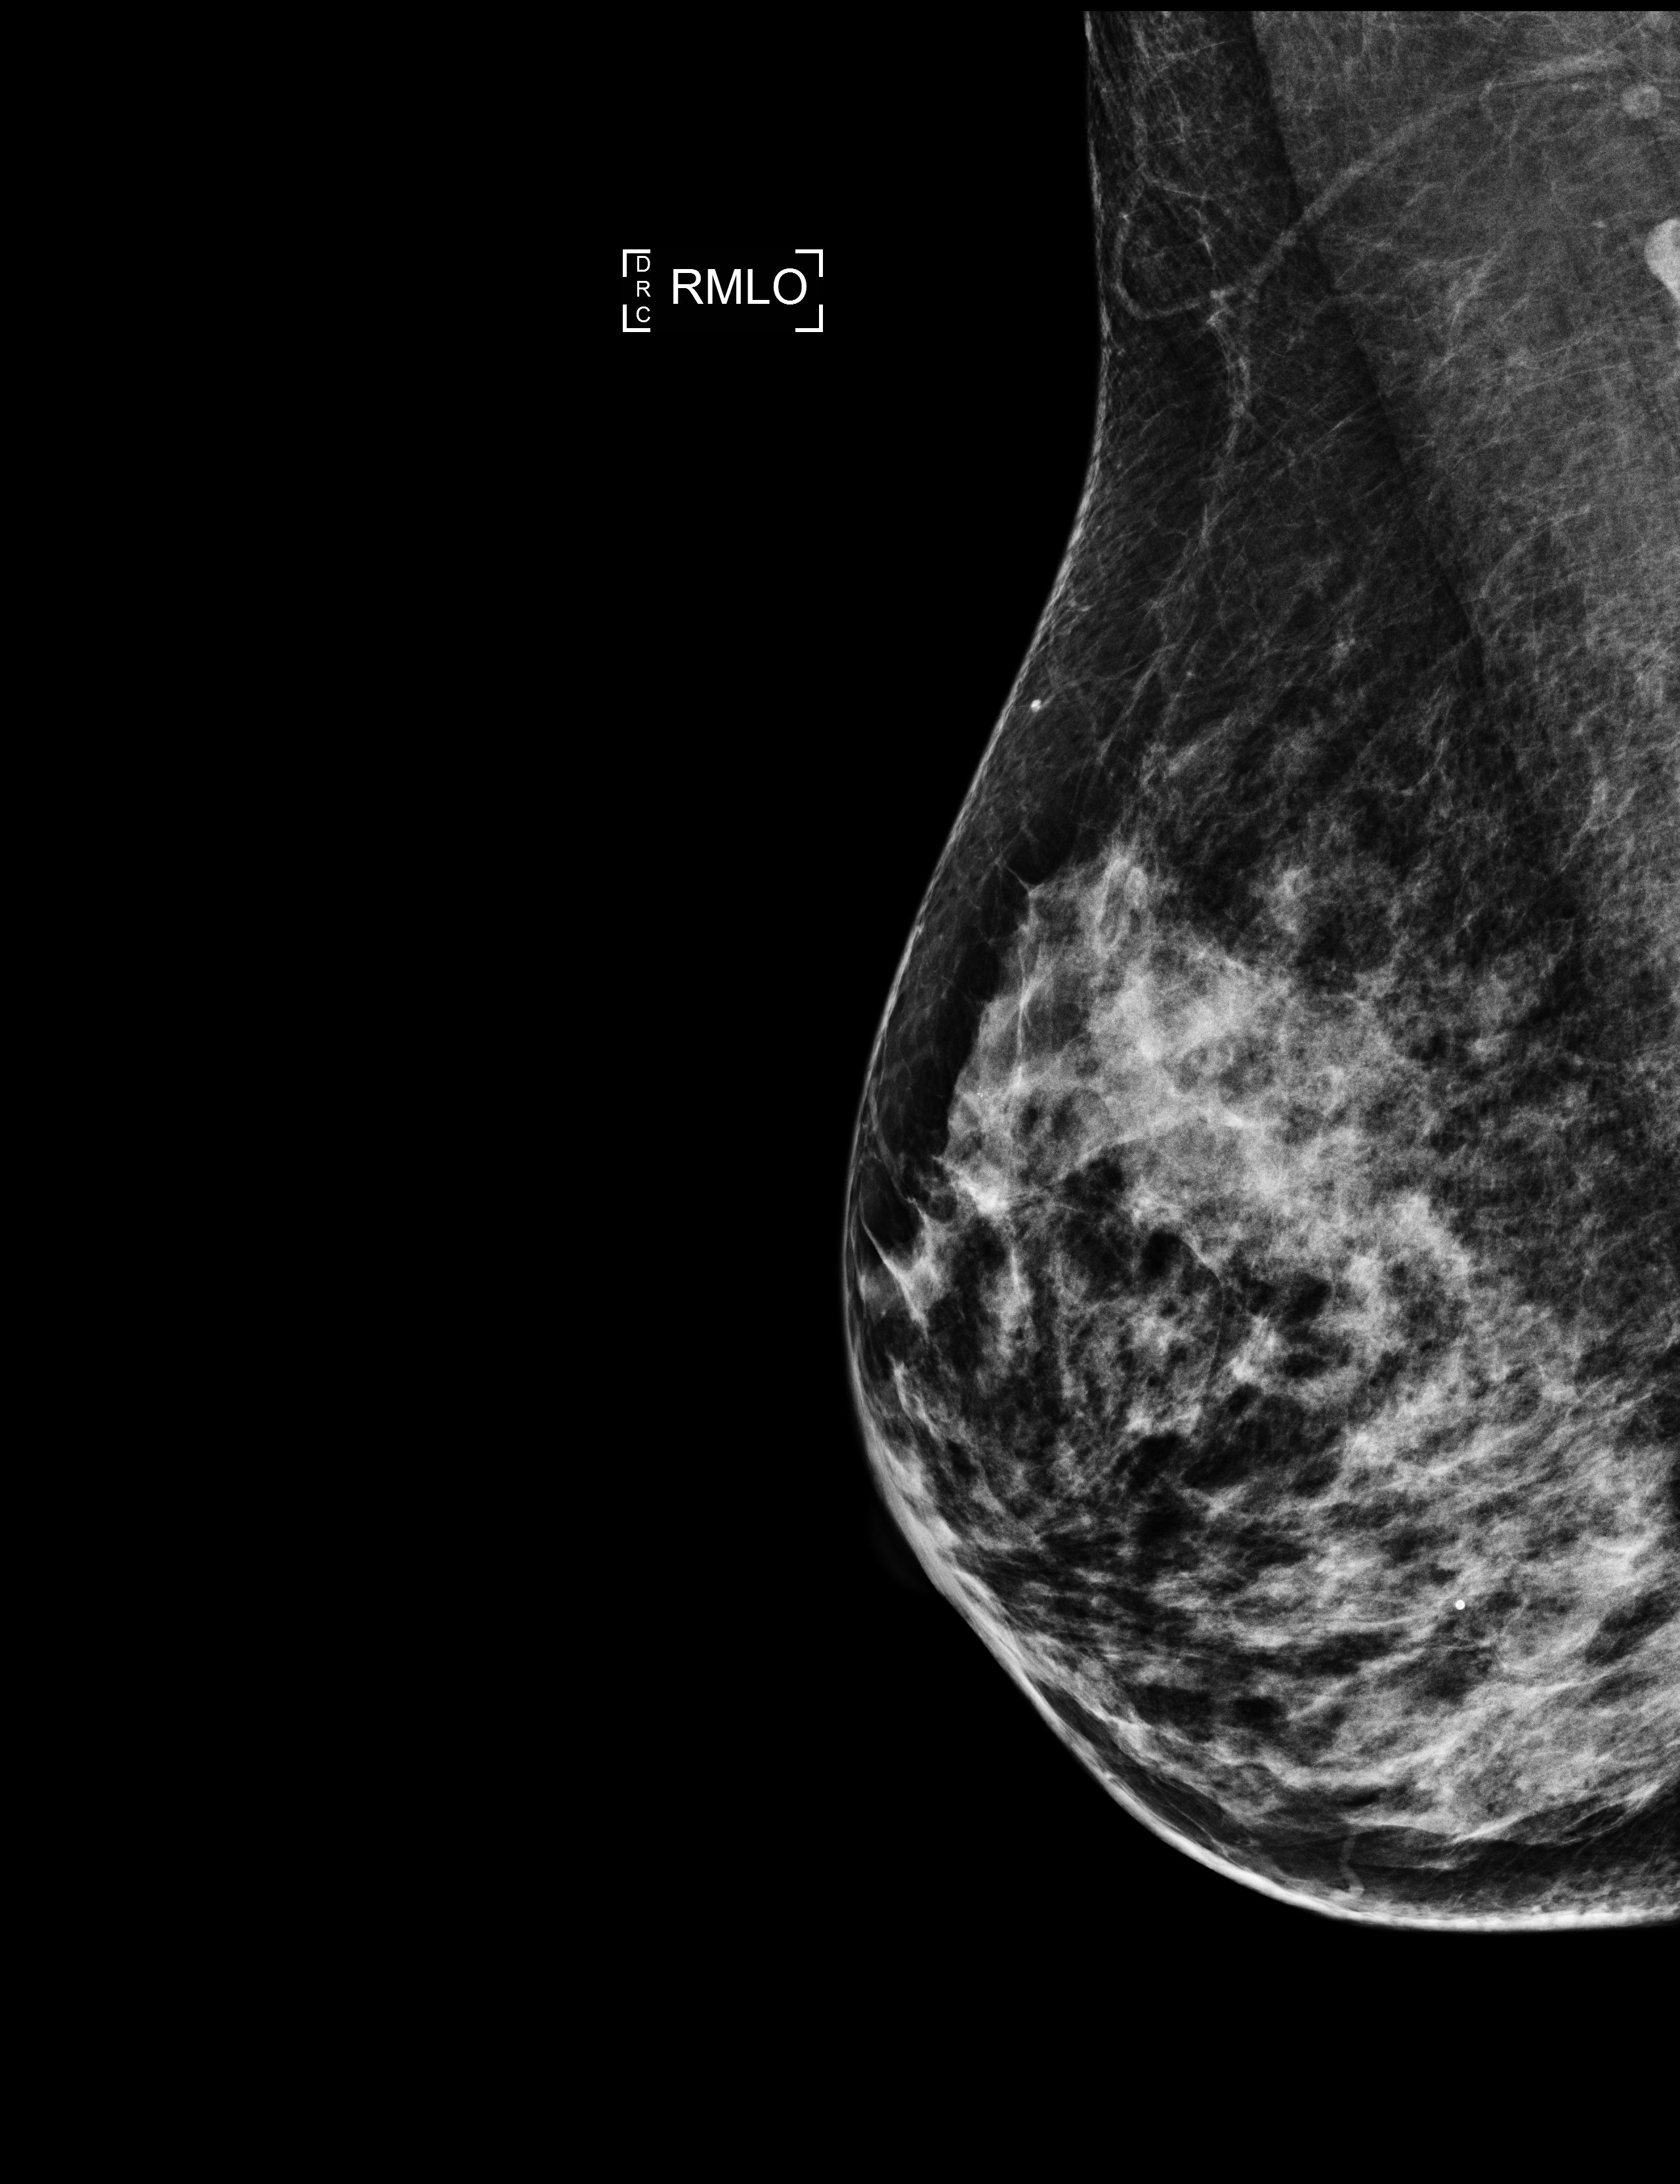
Full-field digital mammogram (FFDM), right breast, MLO view, screening examination, compressed breast thickness 50 mm, system: Selenia Dimensions. Patient: female, 60 years.
Final BI-RADS assessment for this screening round (tomosynthesis exam, both breasts): category 1.